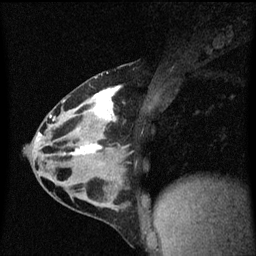
Breast MRI (dynamic contrast-enhanced), one sagittal slice; position 30 of 60 along the scan axis; dynamic contrast-enhanced series, image 2 of 3 at this slice position (ordered by acquisition); 1.5 T; TE 4.2 ms, TR 8.4 ms; 256 × 256 image matrix, field of view 200 × 200 mm. Female patient, age 32 years.
Annotated regions visible in this slice (semi-automatically segmented with operator editing):
- analysis volume of interest (the breast-tissue region the enhancement analysis was run in; not a lesion): box from (x=34, y=74) to (x=146, y=169) px
- tumour enhancement mask (voxels above the 70 % enhancement threshold inside the analysis volume of interest): (x=50, y=86)–(x=122, y=155)